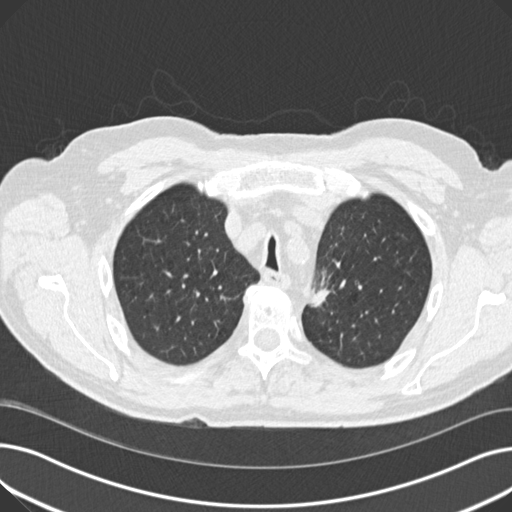
Chest CT (low-dose screening protocol), one axial image, third screening round (two years after baseline), lung window (W 1500 / L -600 HU), 2 mm slice thickness, standard (soft-tissue) reconstruction kernel (B30f), 120 kVp, slice 47 of 191 in the series. Male participant, aged 70 years at enrolment.
Expert-annotated lung lesion, bounding box [x1, y1, x2, y2] px = [303, 267, 342, 310]. The screening reader recorded 2 non-calcified nodules or masses ≥4 mm on this exam (left upper lobe, left lower lobe); which of them this box marks is not recorded. Official screen result: positive, other. Participant outcome: lung cancer diagnosed 175 days after this screen — mixed cell adenocarcinoma, left upper lobe, poorly differentiated (G3), stage IIB (AJCC 6th edition), 17 mm at pathology.